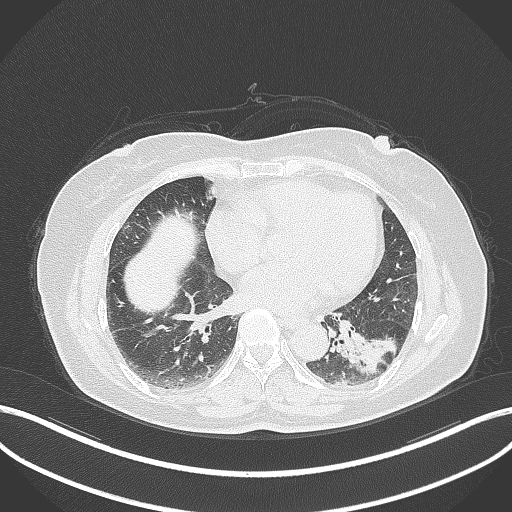
Chest CT, one axial slice; position 152 of 311 along the scan axis; reconstruction kernel B70f; 120 kVp; lung window (W 1500 / L -600 HU); 1 mm slice thickness; 512 × 512 image matrix, field of view 400 × 400 mm. Patient: female, 59 years. Case-level facts recorded for this patient, not image findings: clinical TNM (as recorded): T2a N0 M0; histopathological grade: G2-3.
Structures marked on this image (rectangle marked by the reading radiologist):
- lung tumour (recorded histology: adenocarcinoma): bounding box (x1, y1, x2, y2) in pixels: (346, 325, 398, 378)